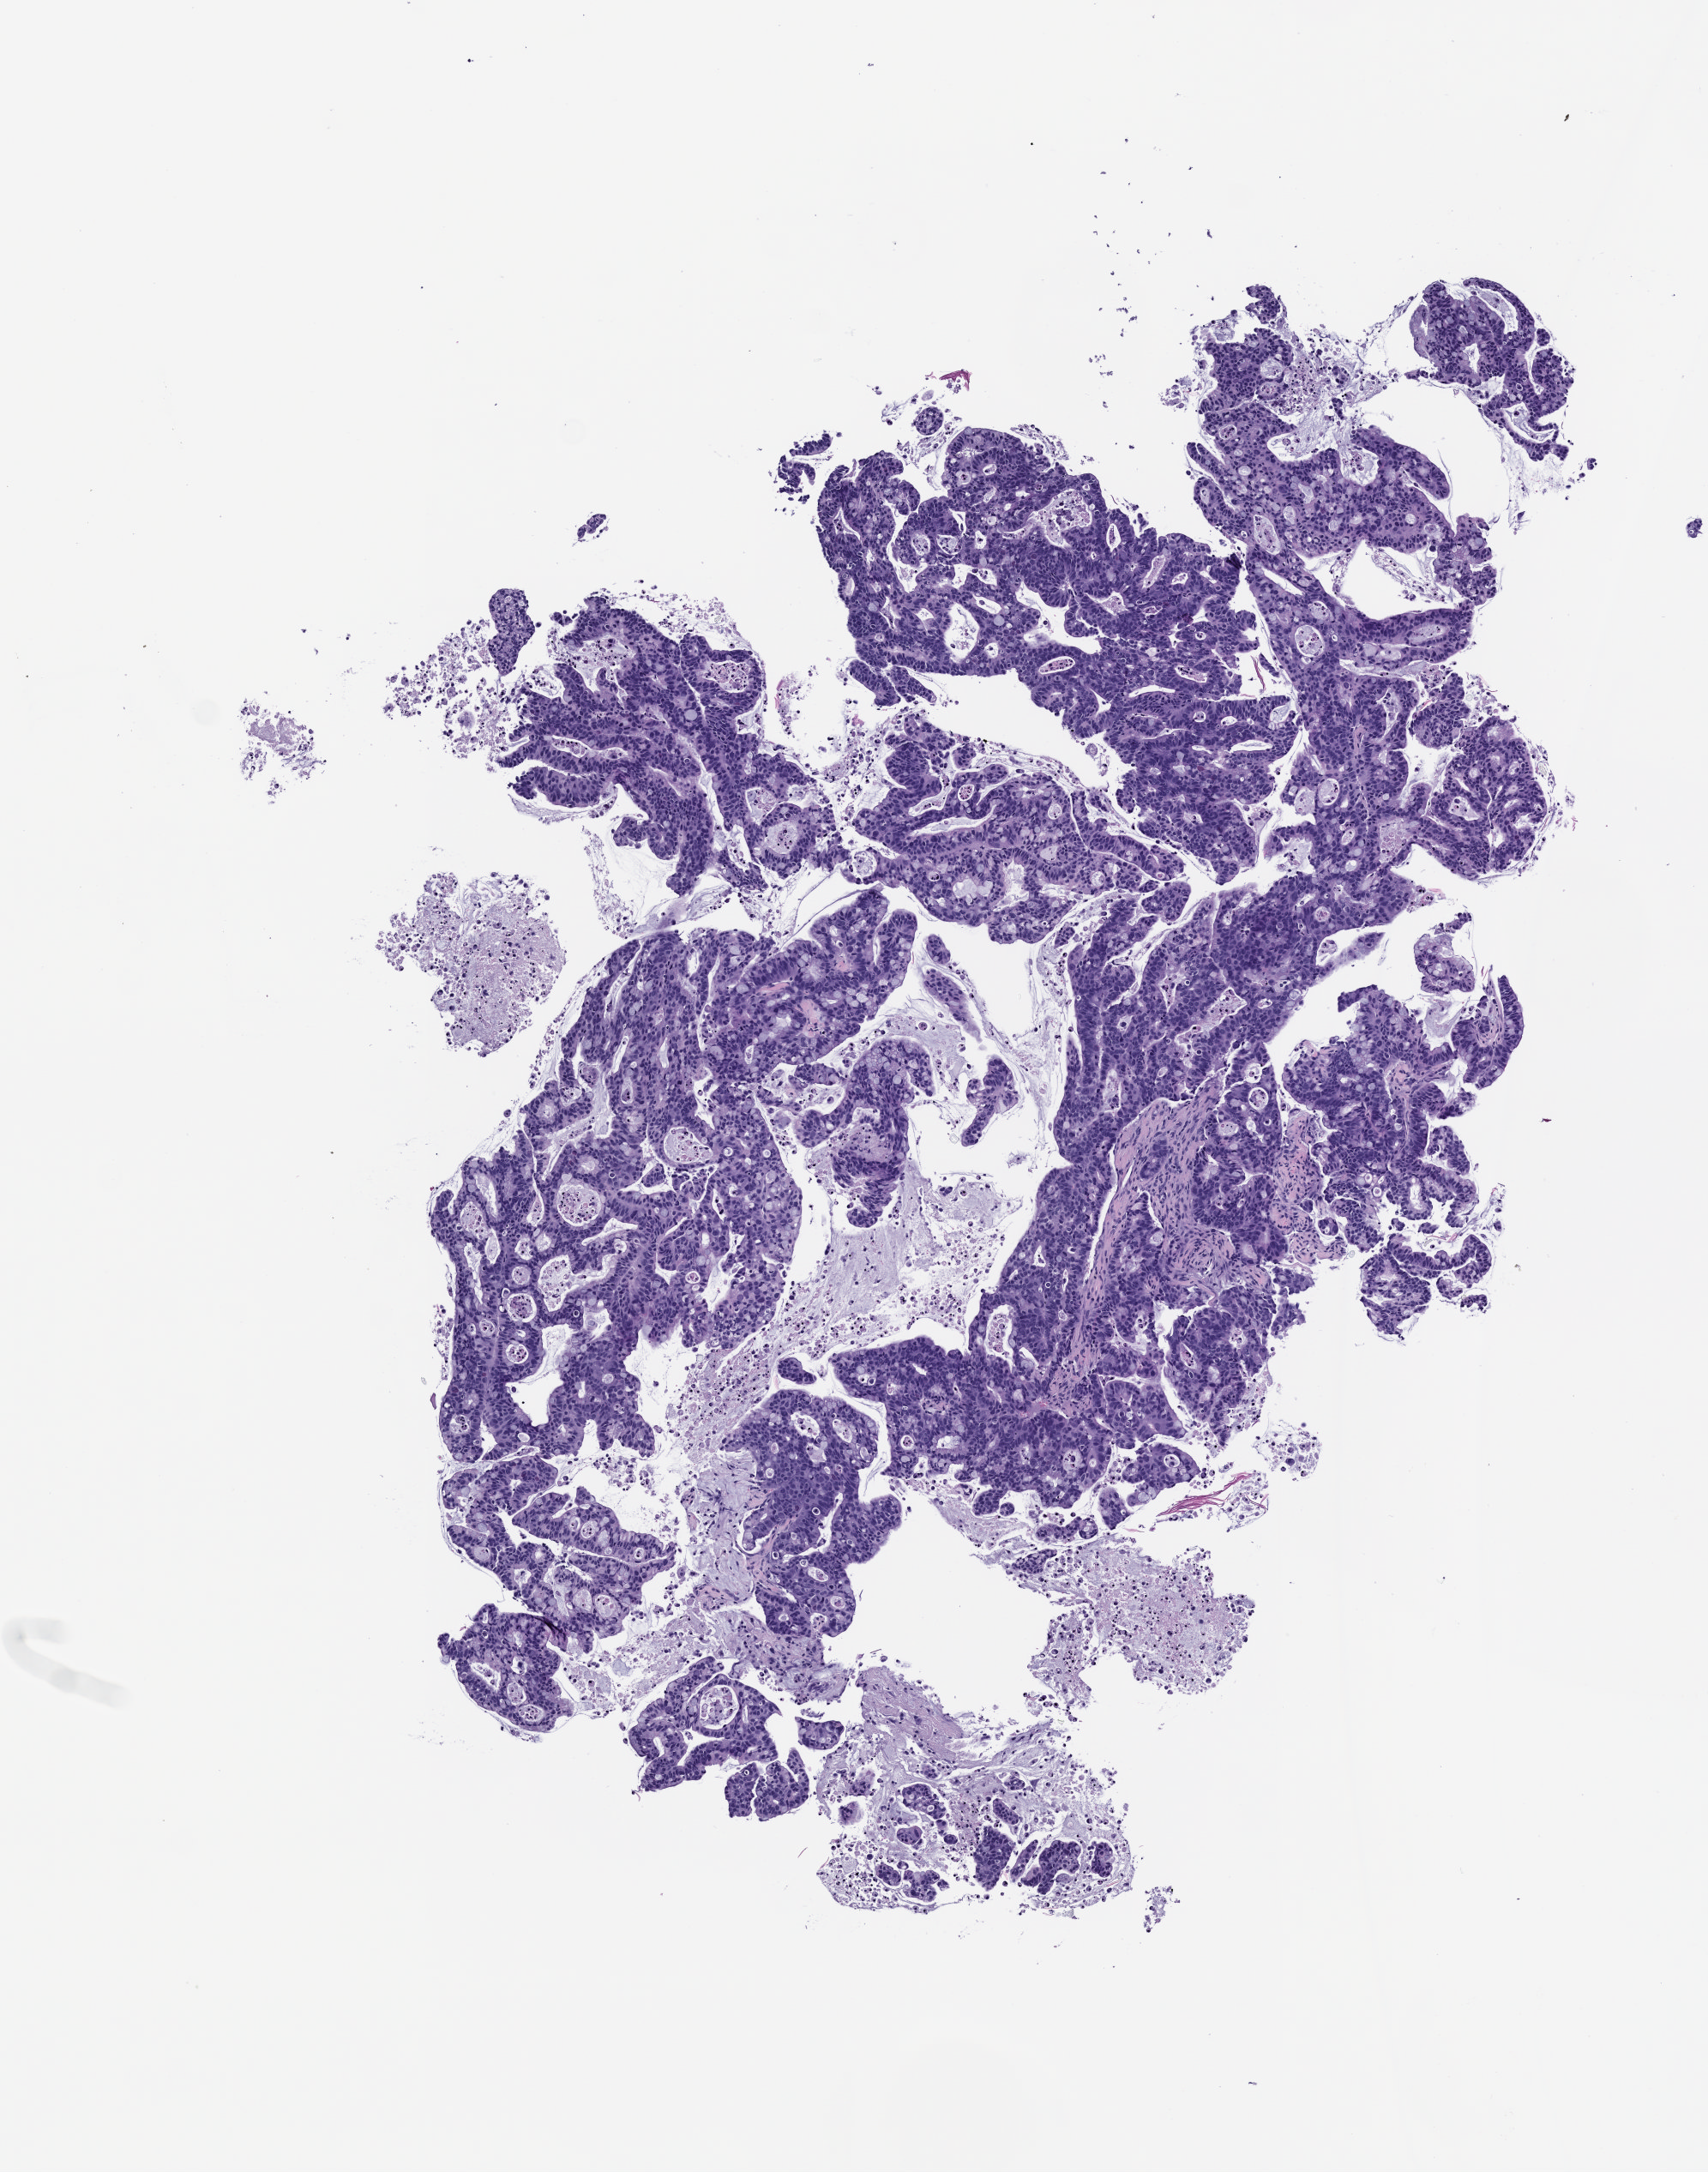
Haematoxylin and eosin whole-slide image of a patient-derived xenograft (PDX) tumor grown in a mouse — shown as a low-resolution overview of the whole scanned area (about 4.0 x 5.1 mm). Formalin-fixed paraffin-embedded section. Tumor site category: small intestine.
• originating patient diagnosis: Small Intestinal Adenocarcinoma